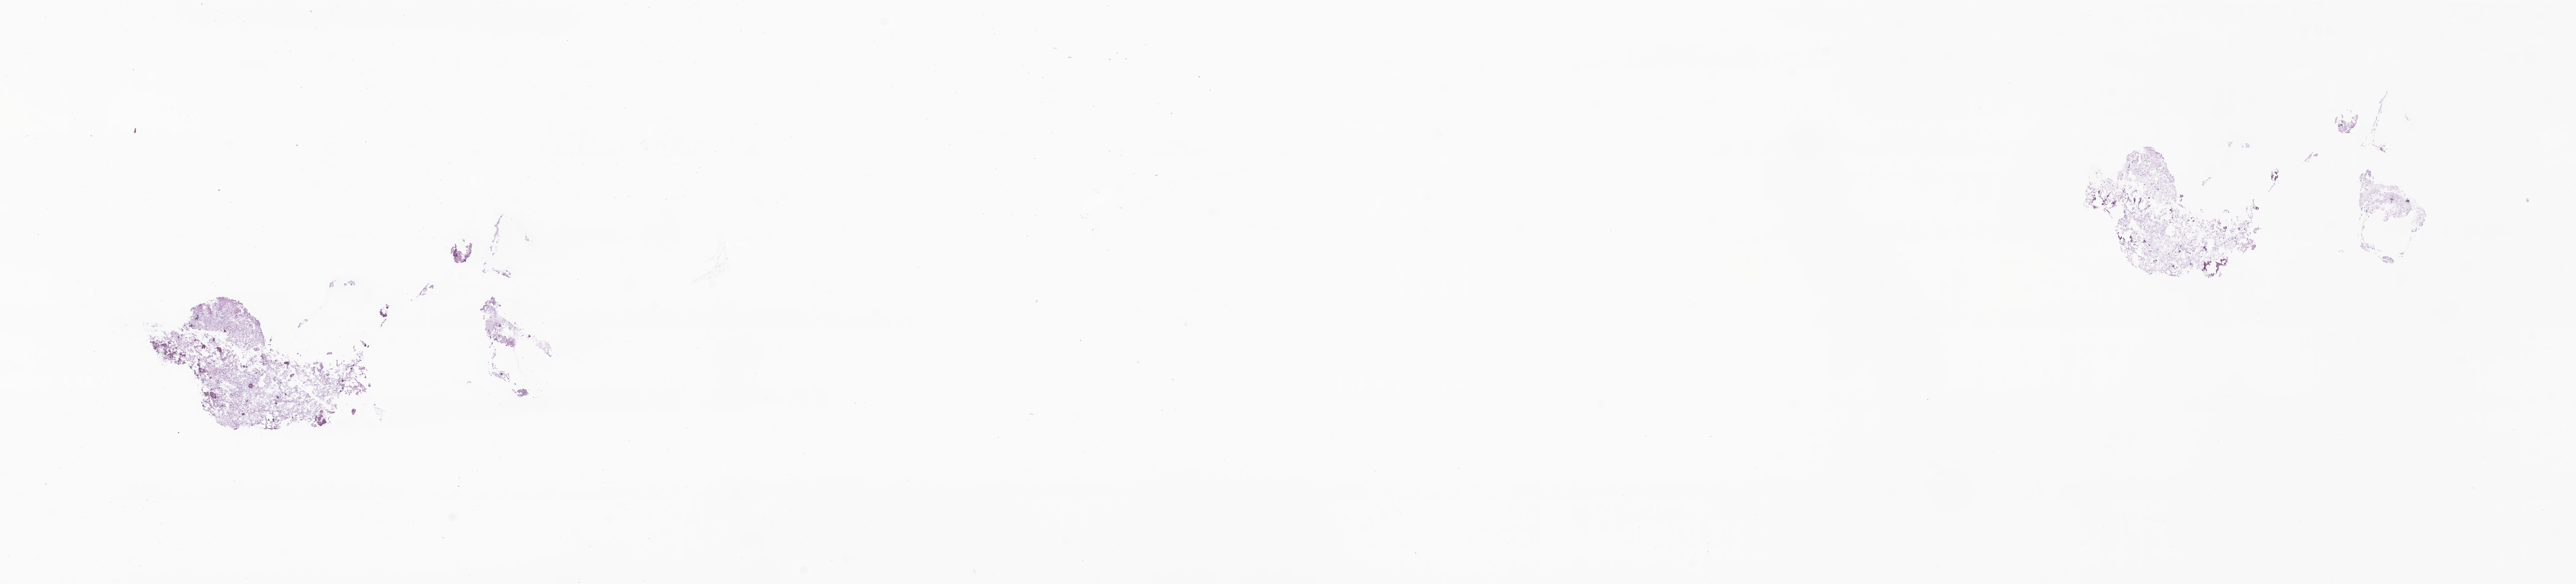
Digitized H&E-stained section of tumor tissue from the brain, shown as a low-resolution overview of the whole scanned area (about 32.1 x 7.3 mm); cryosection (OCT / tissue freezing medium). Patient male; age 135 months (11 years 3 months).
Recorded diagnosis: Neoplasm, malignant.